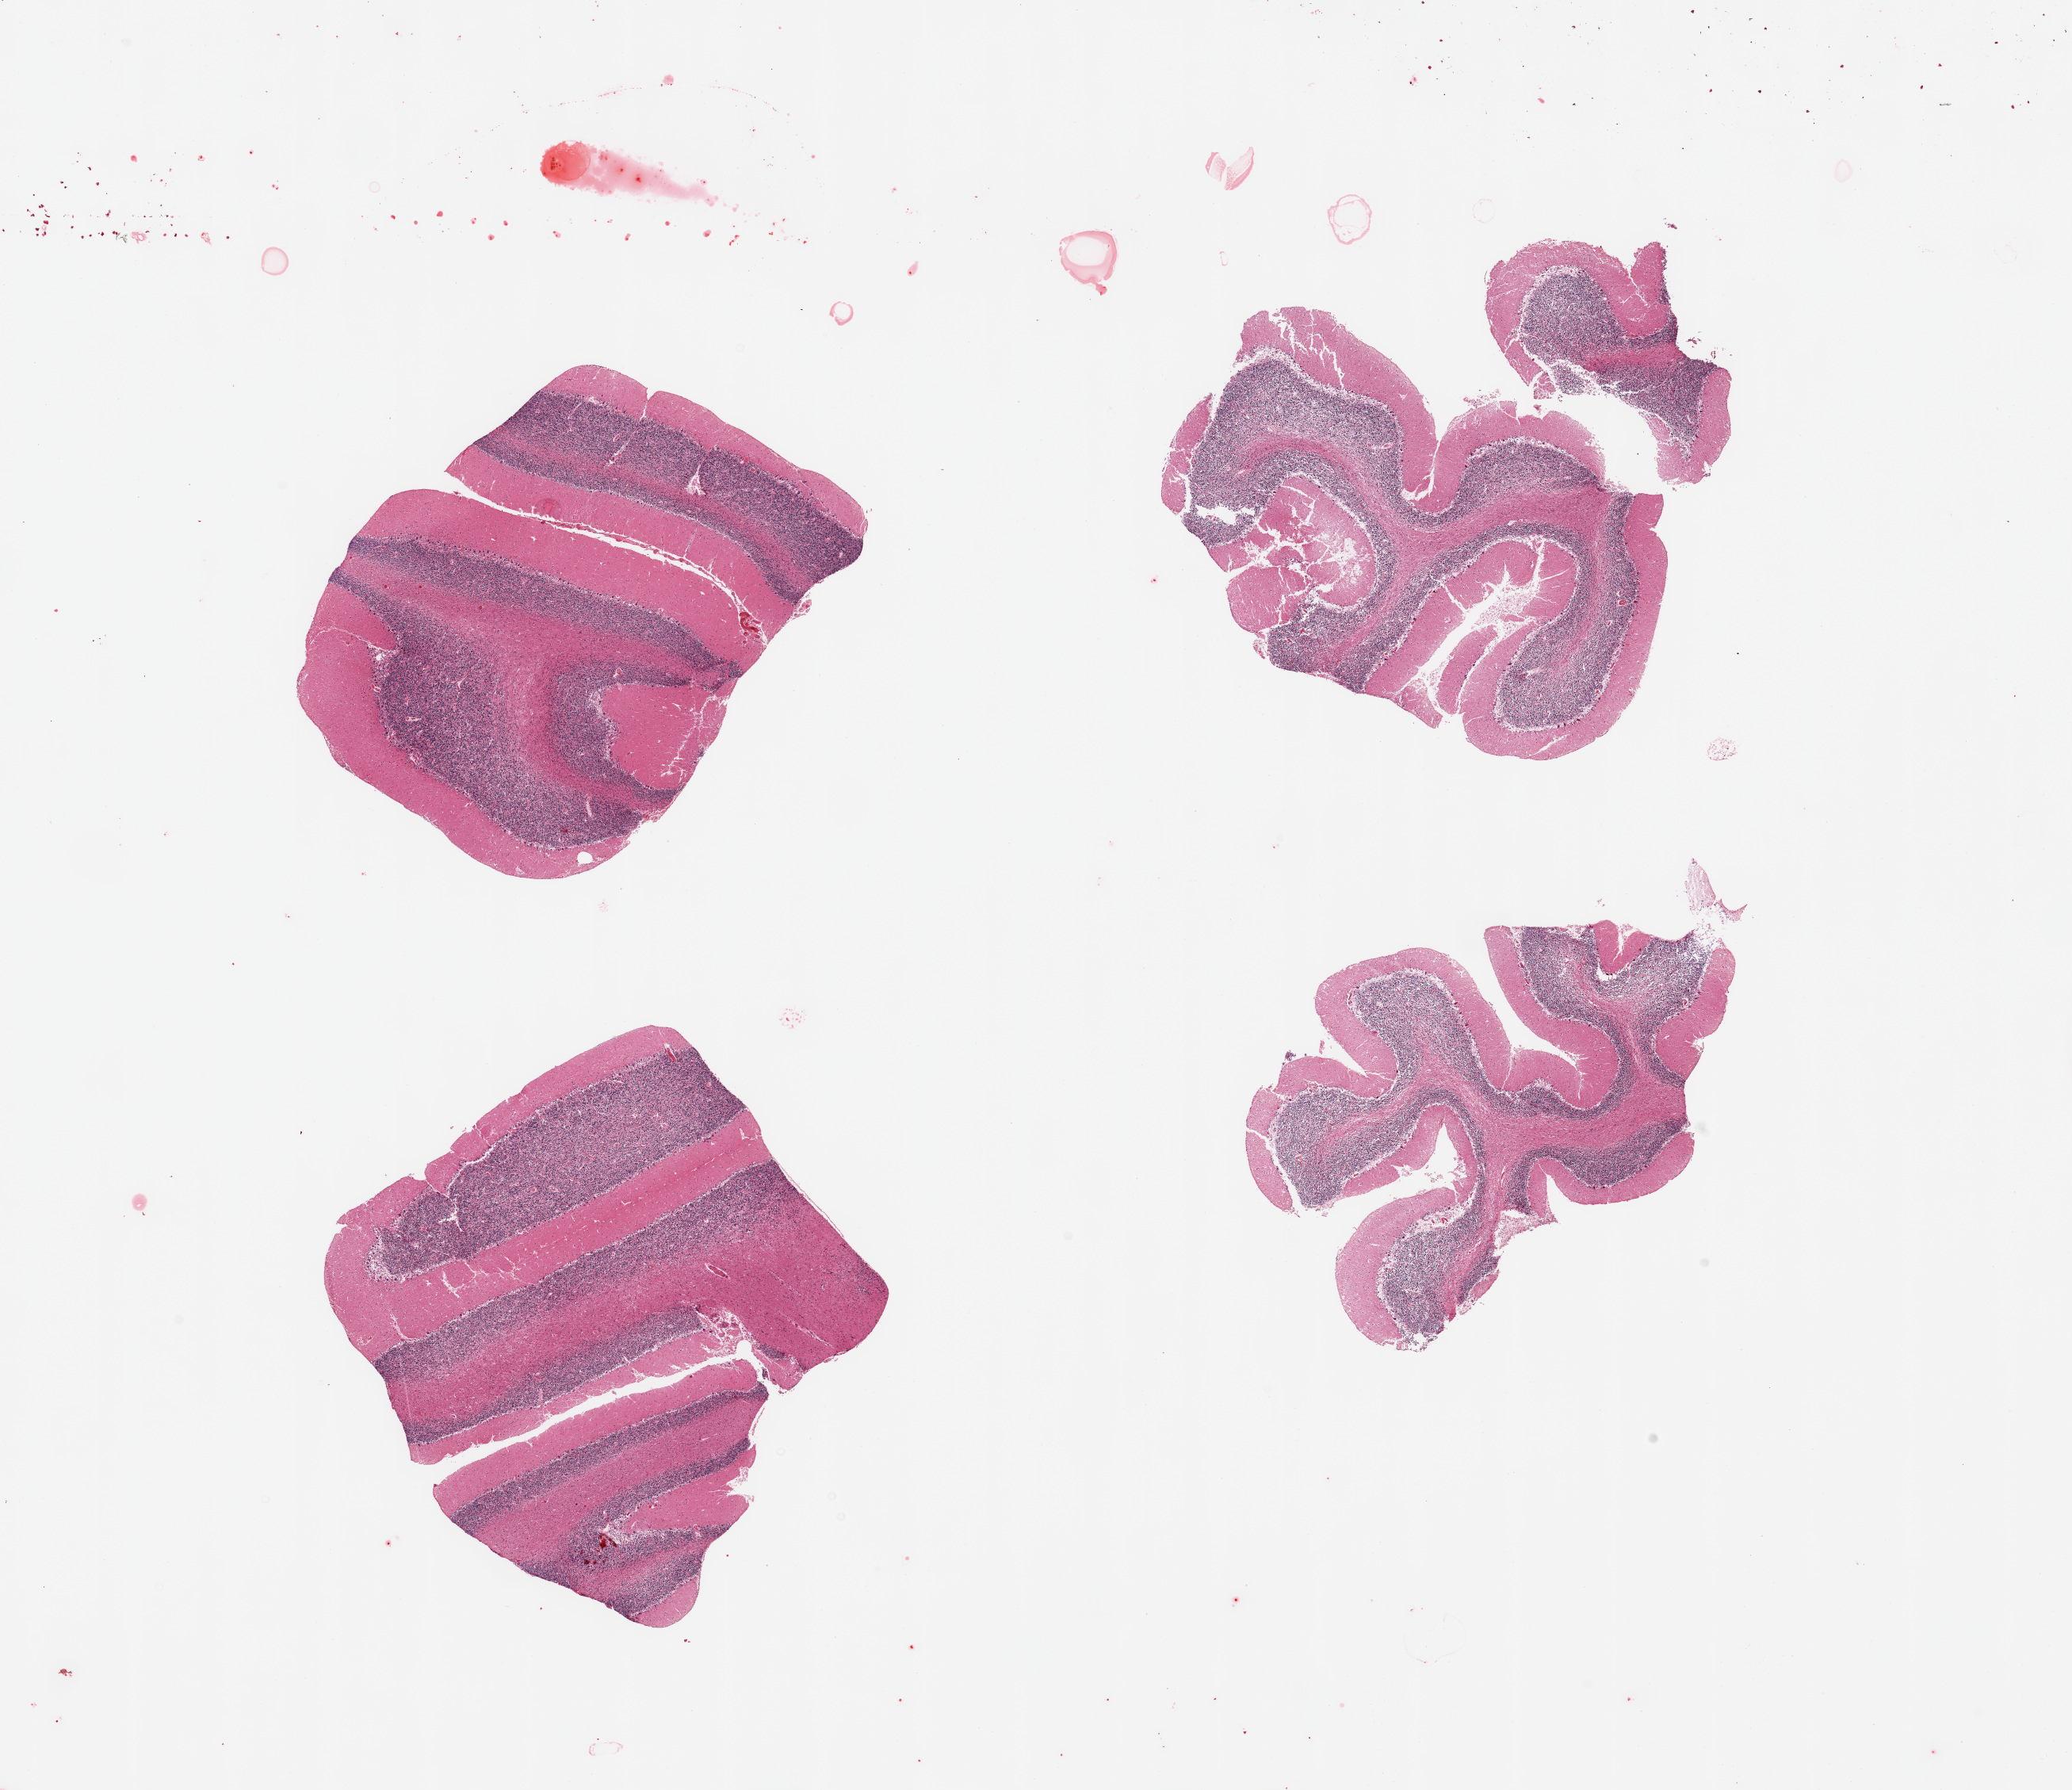
Whole-slide image, hematoxylin and eosin (H&E) stain, brightfield, whole scanned area (about 20.7 x 17.9 mm) shown as a low-resolution overview. PAXgene-fixed, paraffin-embedded tissue. Sampled site (target tissue): cerebellum. Tissue donor sample. Female donor.
Reviewer comment on this tissue sample: 4 pieces; autolysis varies from piece to piece, 1 to 3.